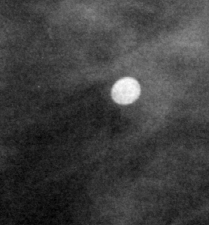
Cropped region of a digitized screen-film mammogram centred on a radiologist-marked abnormality; right breast; CC view; BI-RADS breast density category 2 (scale 1–4).
Calcifications, morphology lucent center; BI-RADS assessment category 2; benign without callback (not worked up further).